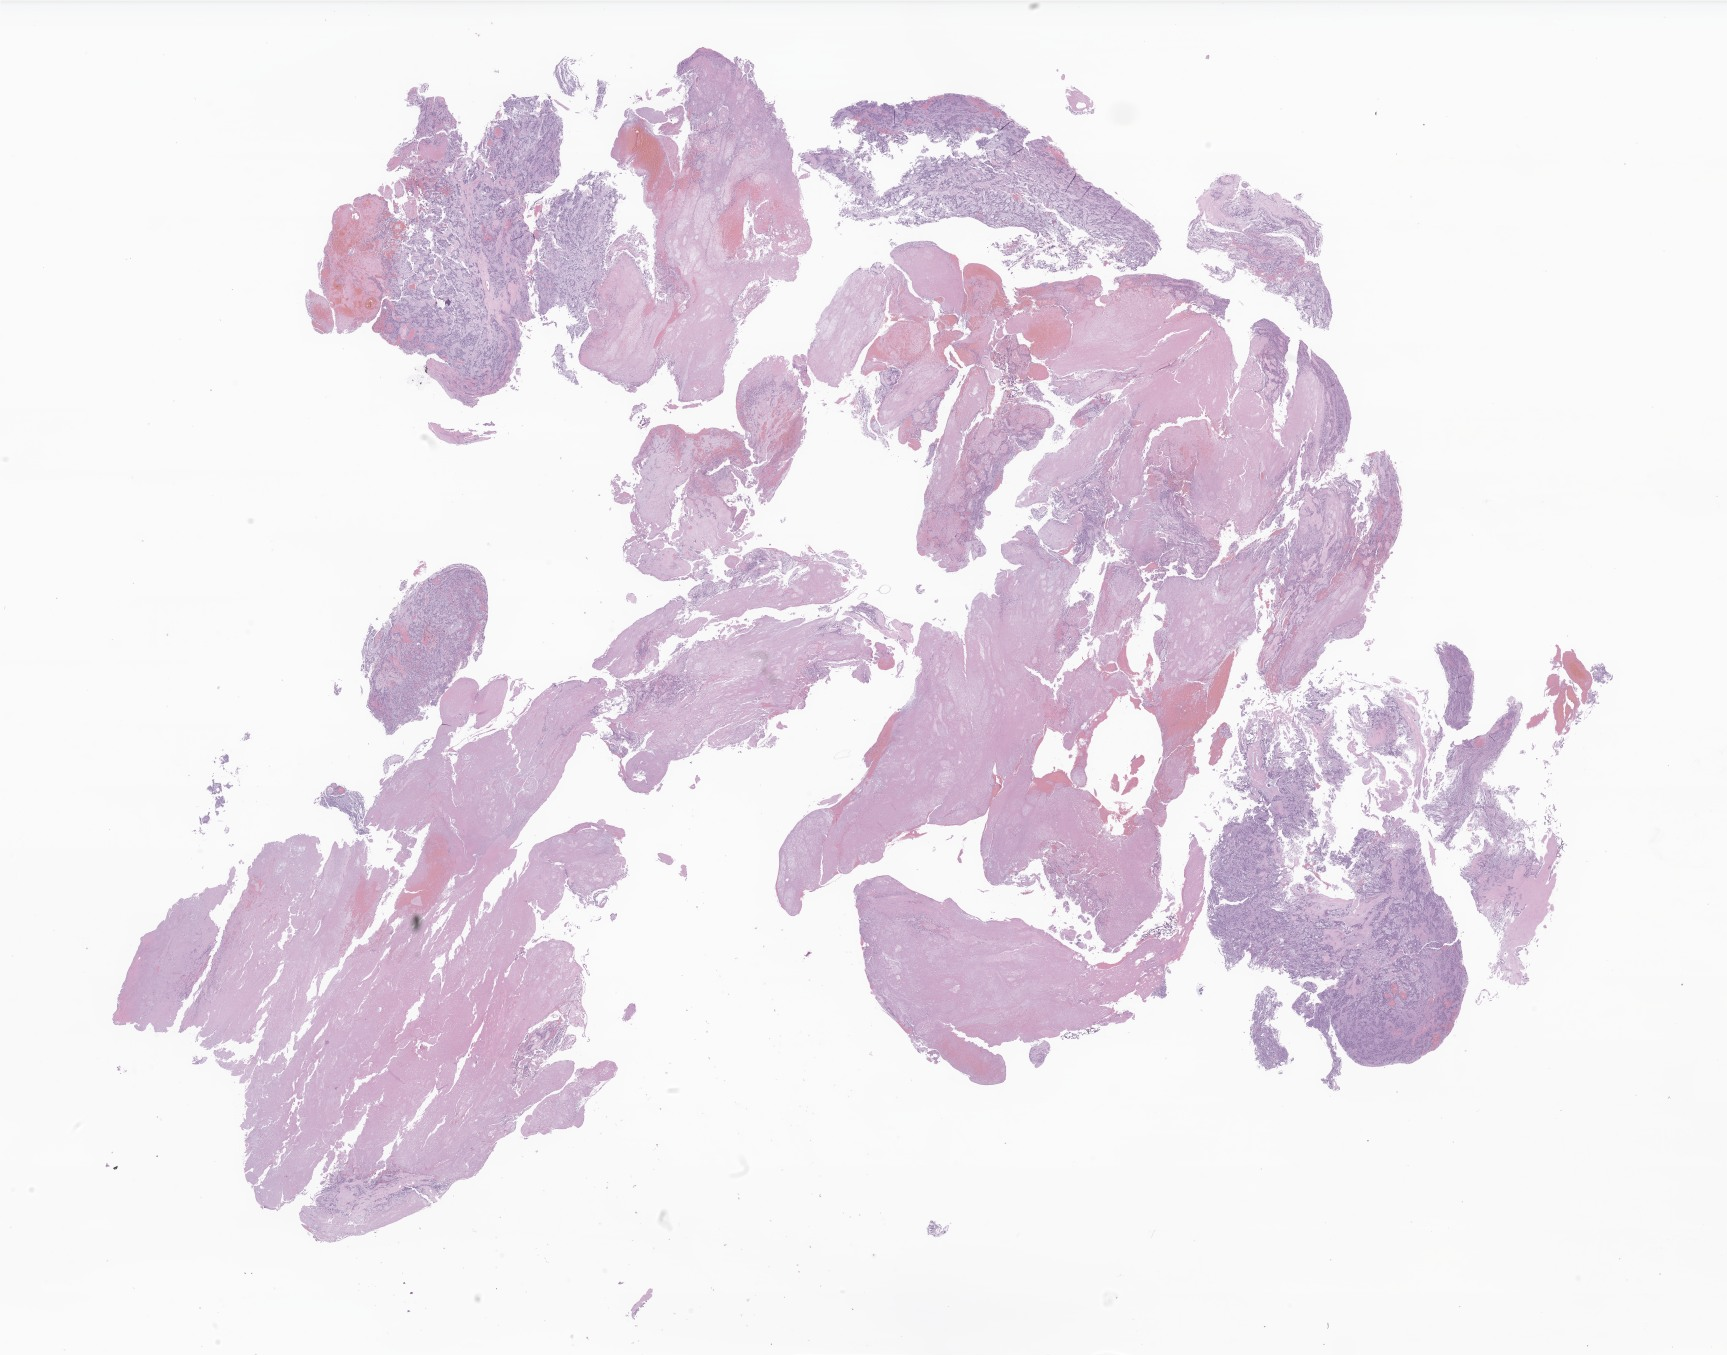
Digitized H&E-stained section of tumor tissue from the spinal cord — whole scanned area (about 29.1 x 22.9 mm) shown as a low-resolution overview; formalin-fixed, paraffin-embedded (FFPE) tissue. Patient male; age 148 months (12 years 4 months).
- diagnosis: Neoplasm, malignant